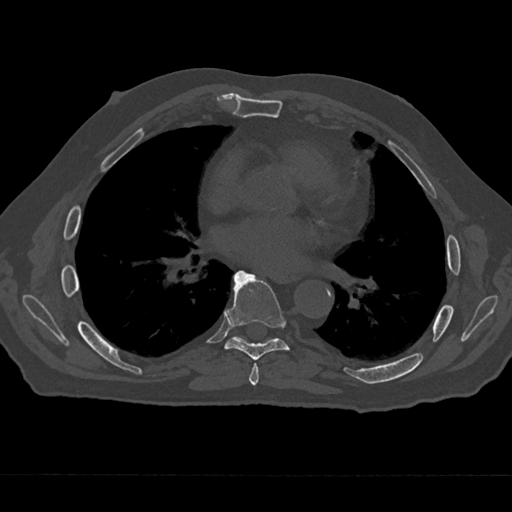
CT including the spine, one axial slice. Slice 366 of 797 in the series (ordered by position). Reconstruction kernel Br40s/3. Bone window (W 1800 / L 400 HU). 0.5 mm slice thickness. 512 × 512 image matrix, field of view 377 × 377 mm. Male patient, age 75 years. Case-level facts recorded for this patient, not image findings: primary cancer: renal; vertebrae with lytic lesions (as recorded): T4.
Annotated regions visible in this slice (semi-automatic segmentation, software-assisted and operator-edited):
- T6 vertebra: bounding box [x1, y1, x2, y2] px = [249, 363, 259, 385]
- T7 vertebra: [226, 271, 289, 360]